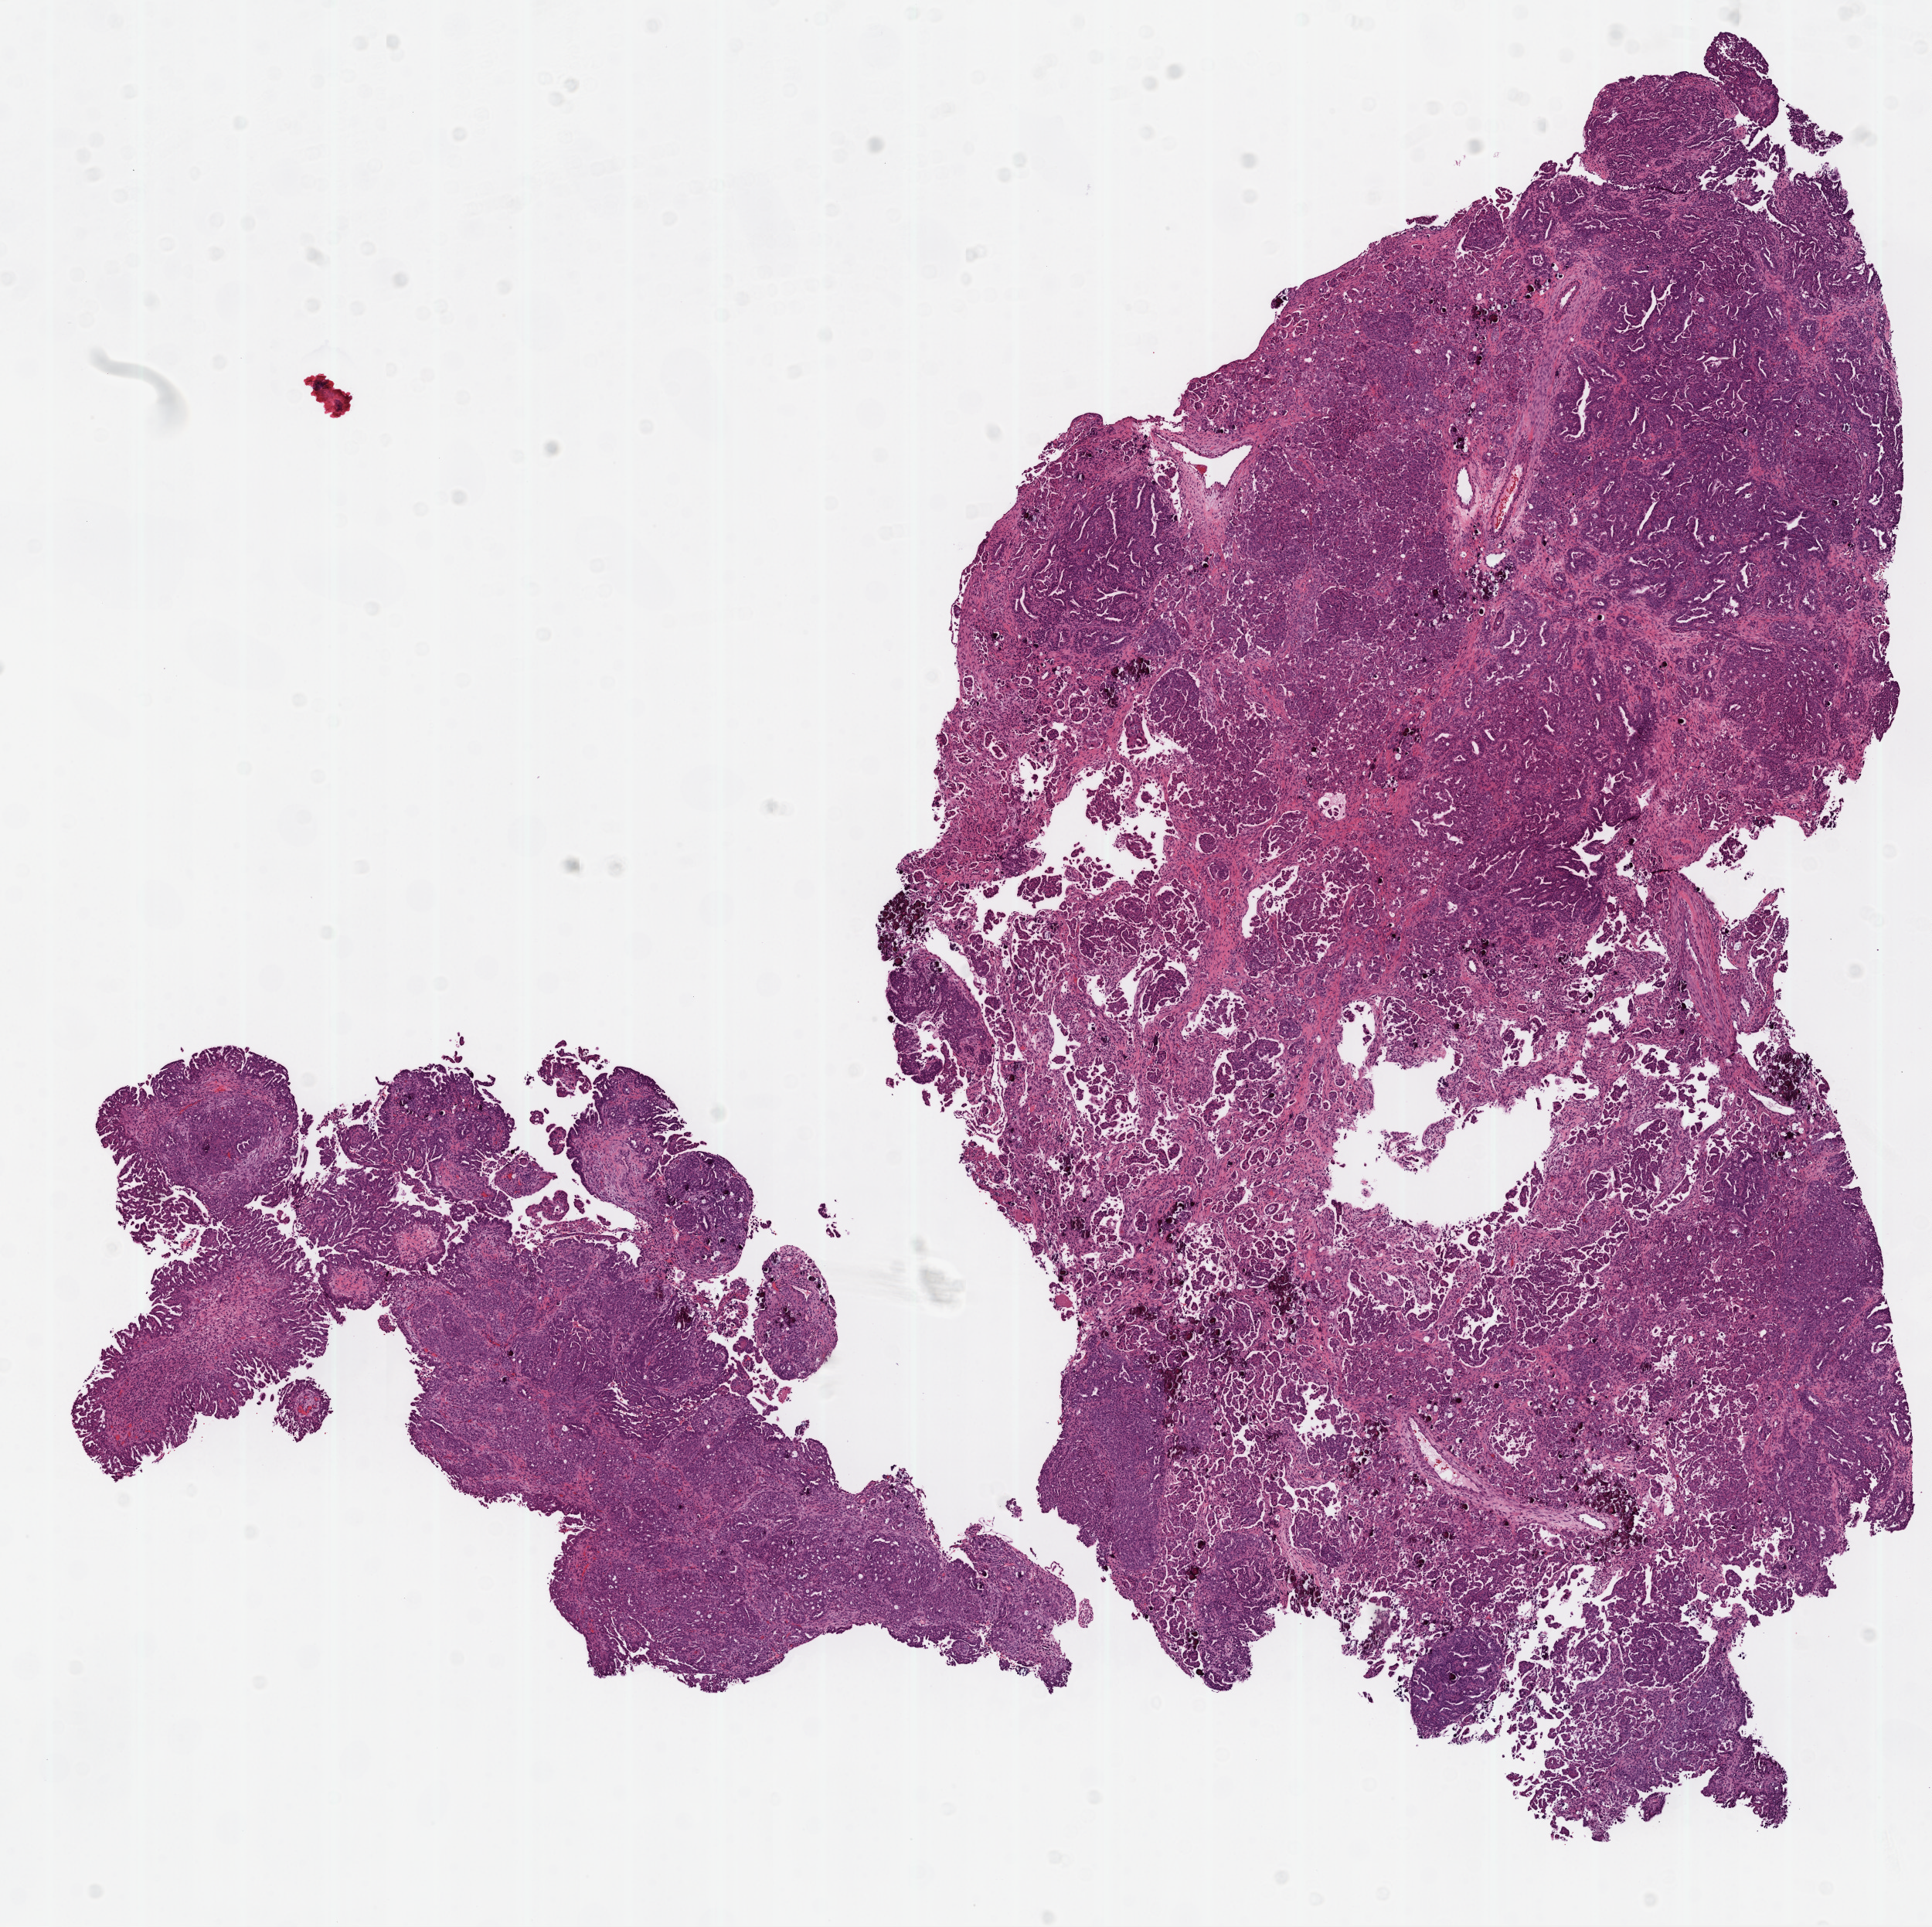
Digitized Hematoxylin and eosin (H&E) stained tissue section (whole slide), low-resolution overview of the scanned area, about 10.0 x 10.0 mm (slide scanned at 20x), frozen section, primary tumour sample from the ovary. Patient: female, age at initial diagnosis 57 years. Histologic grade: G2 (moderately differentiated). Pathologist review of this section (percent, as recorded): tumour cells 80%, tumour nuclei 90%, normal cells 0%, stromal cells 20%, necrosis 0%.
- histologic diagnosis: Serous cystadenocarcinoma, NOS
- FIGO stage: IV
- laterality: bilateral